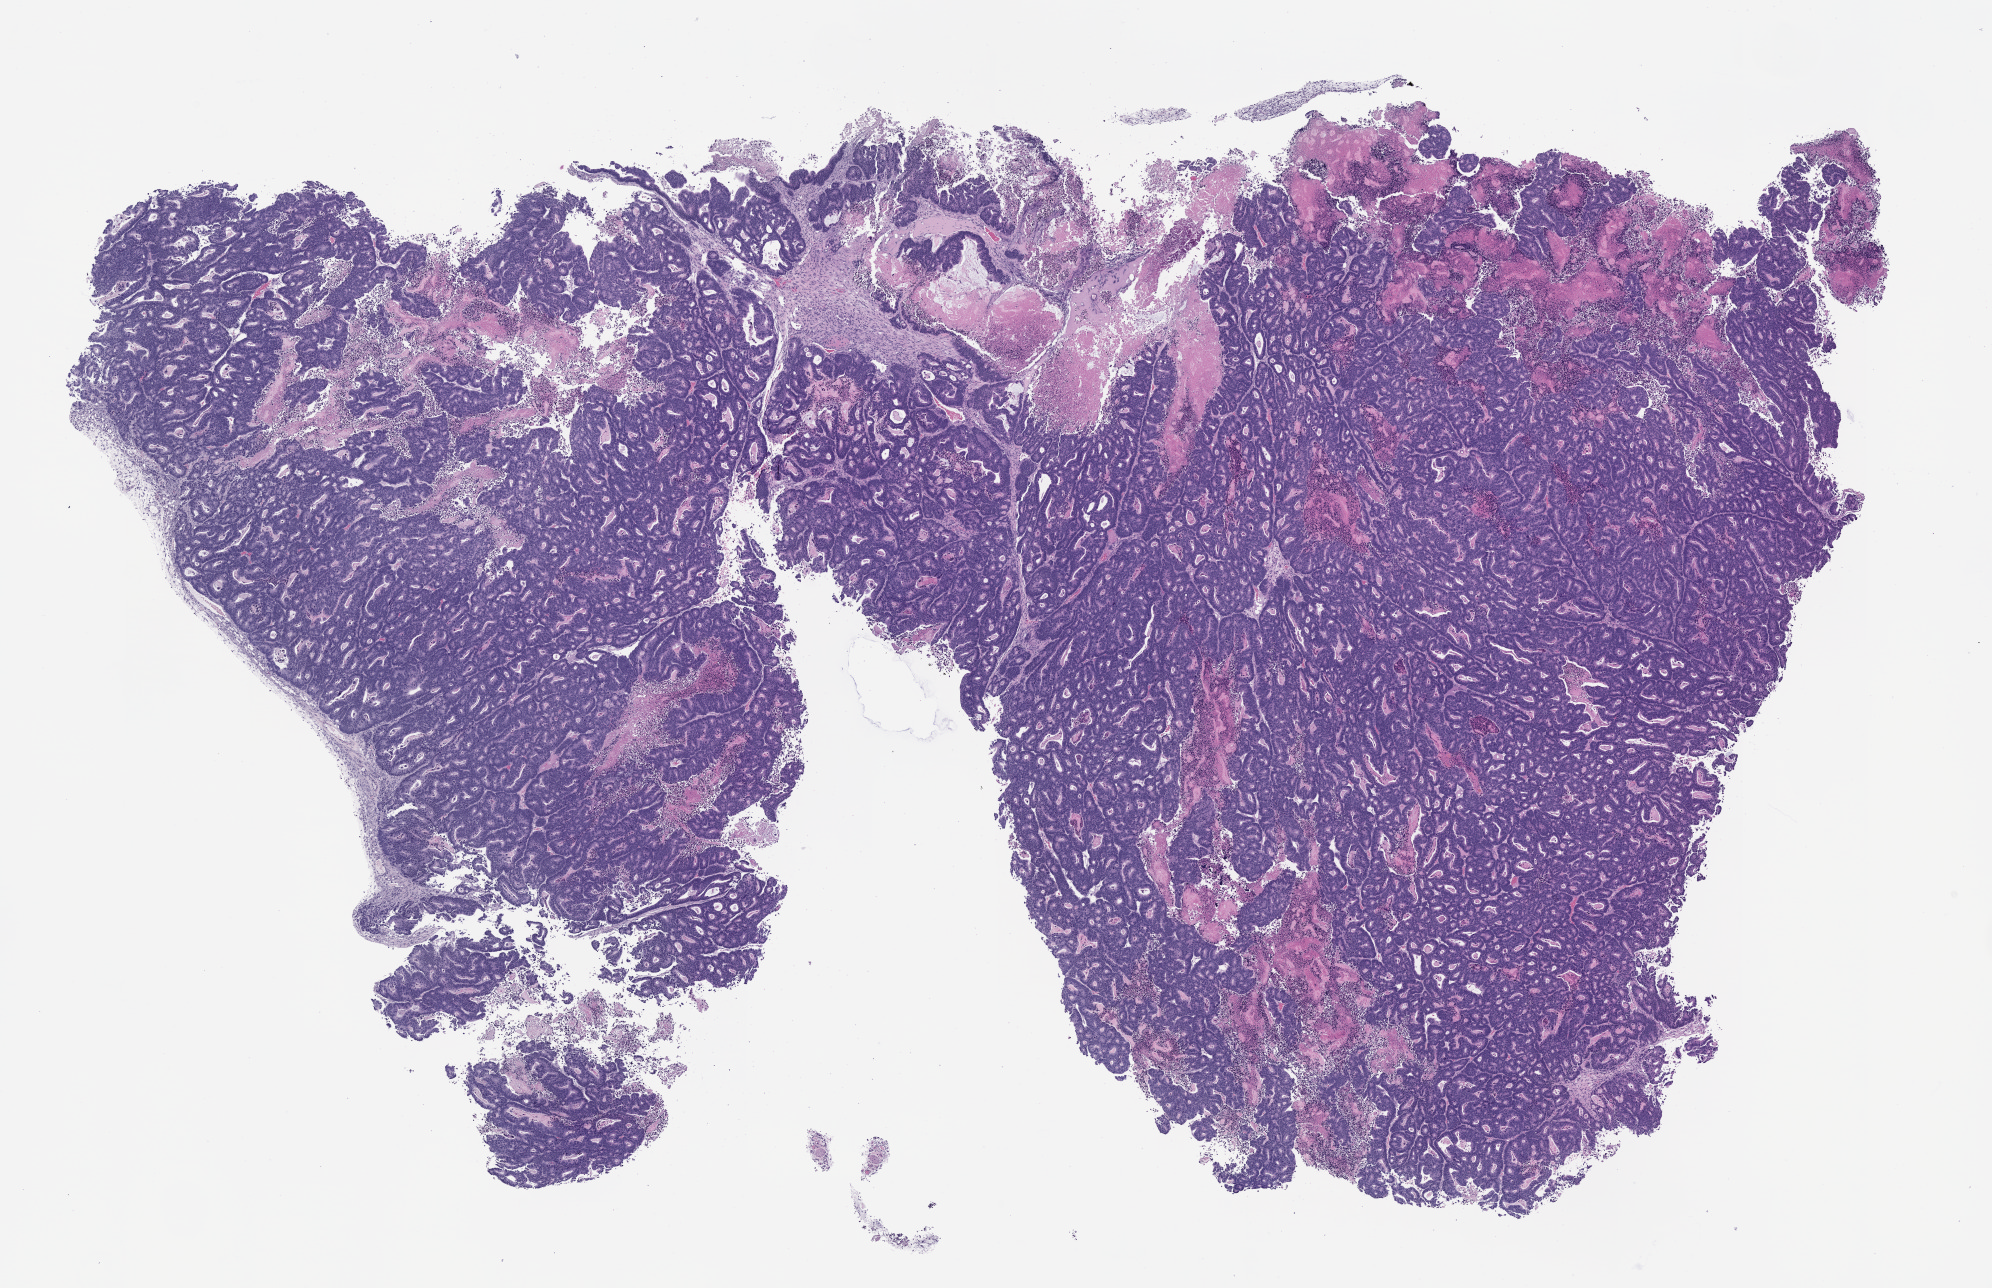
Haematoxylin and eosin whole-slide image of a patient-derived xenograft (PDX) tumor grown in a mouse, passage 0, whole scanned area (about 16.0 x 10.4 mm) shown as a low-resolution overview; formalin-fixed, paraffin-embedded (FFPE) tissue; tumor site category: rectum.
- originating patient diagnosis: Rectal Adenocarcinoma